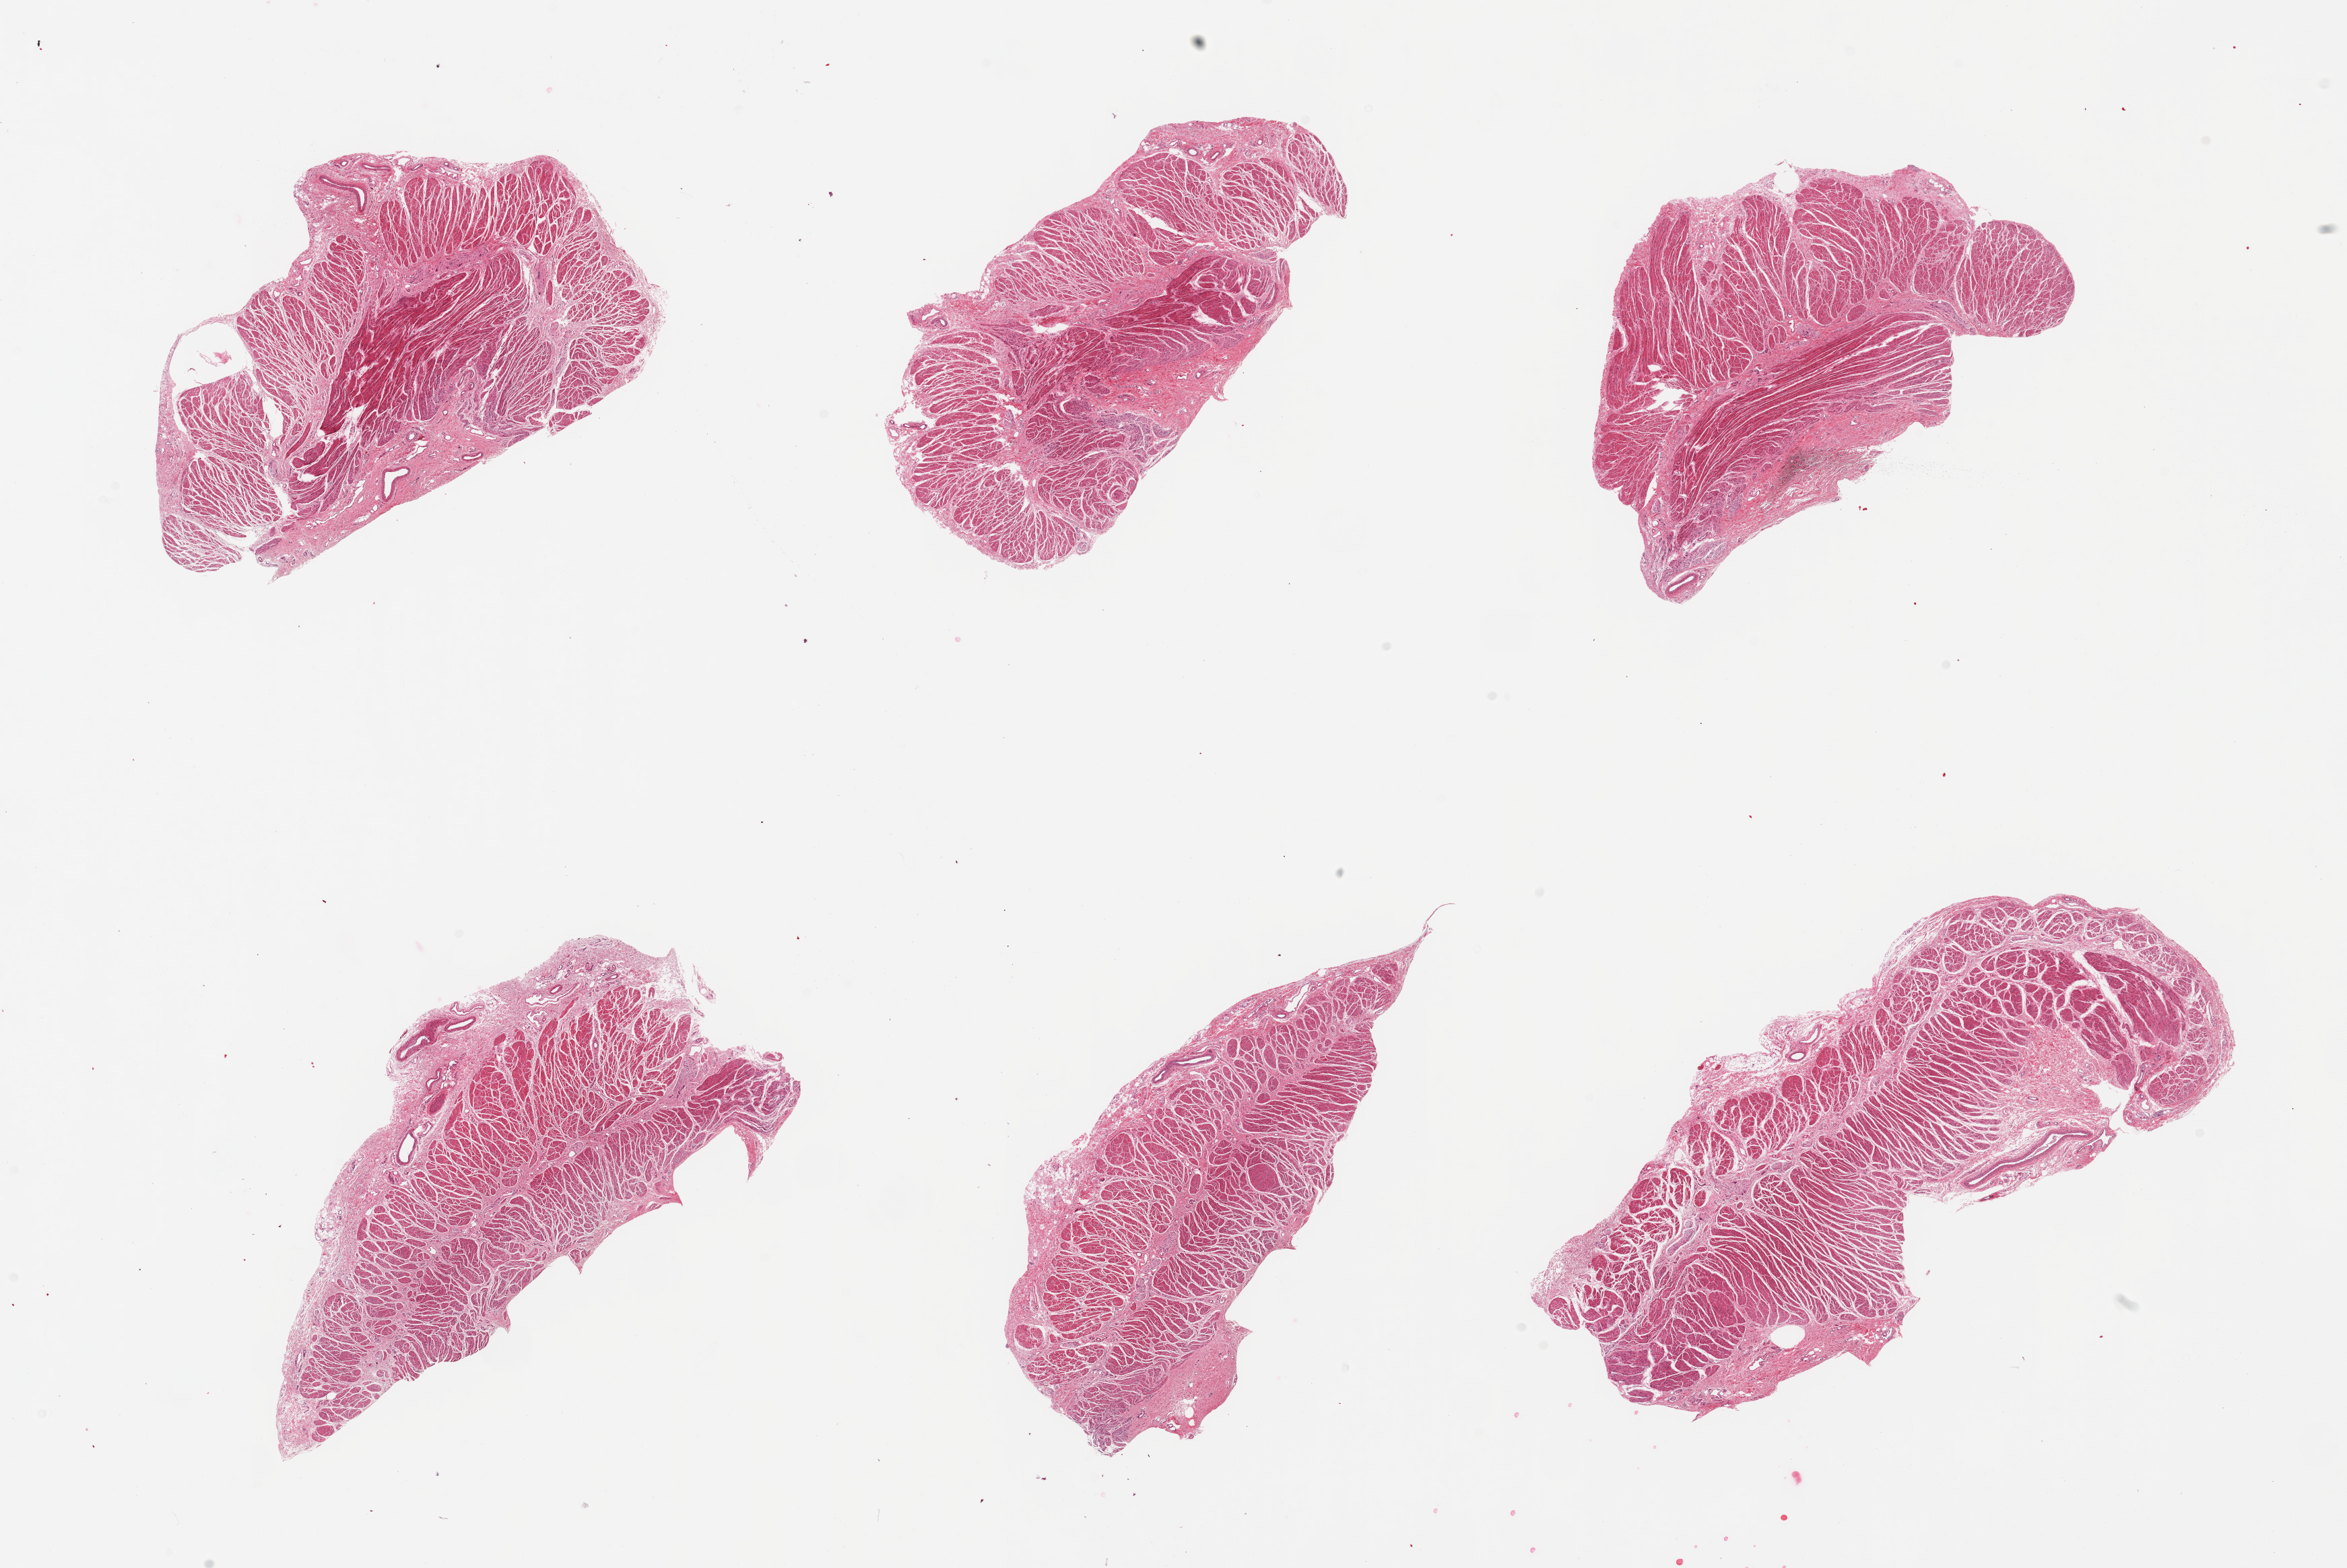
Digitized haematoxylin and eosin-stained section, brightfield, shown as a low-resolution overview of the whole scanned area (about 27.6 x 18.4 mm). PAXgene-fixed paraffin-embedded (PFPE) section. Sampled site (target tissue): gastroesophageal junction. Tissue donor sample.
• review note (as recorded): 6 pieces, all muscularis, good specimens